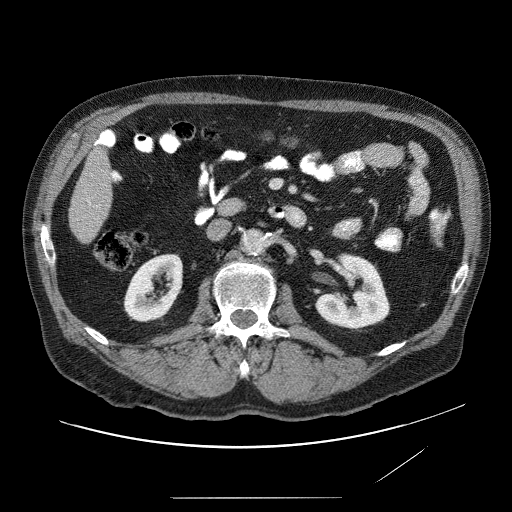
Contrast-enhanced abdominal CT (liver protocol), one axial slice; reconstruction kernel STANDARD; 120 kVp; soft-tissue window (W 400 / L 40 HU); 2.5 mm slice thickness; 512 × 512 image matrix. From the clinical record (not read from this slice): diagnosis: hepatocellular carcinoma (patient treated with transarterial chemoembolisation; whether this scan precedes or follows treatment is not stated here); TNM stage (as recorded): Stage-IVA; Child-Pugh class: A.
Outlined on this slice (semi-automatic segmentation, software-assisted and operator-edited):
- liver parenchyma outside the tumour (the mass and vessels are separate outlines, so this box may not span the whole liver): box from (x=66, y=128) to (x=118, y=246) px
- liver vessels: (x=93, y=128)–(x=108, y=208)